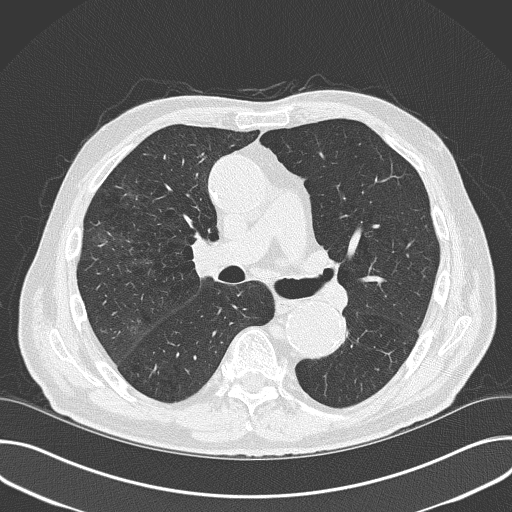
Low-dose screening chest CT, one axial slice; slice 96 of 177 in the series (ordered by position); lung window (W 1500 / L -600 HU); 512 × 512 image matrix, field of view 380 × 380 mm.
Annotated regions visible in this slice (outlined manually by an expert reader):
- lesion 1 (tumor, upper lobe of right lung): bounding box (x1, y1, x2, y2) in pixels: (129, 328, 138, 329)